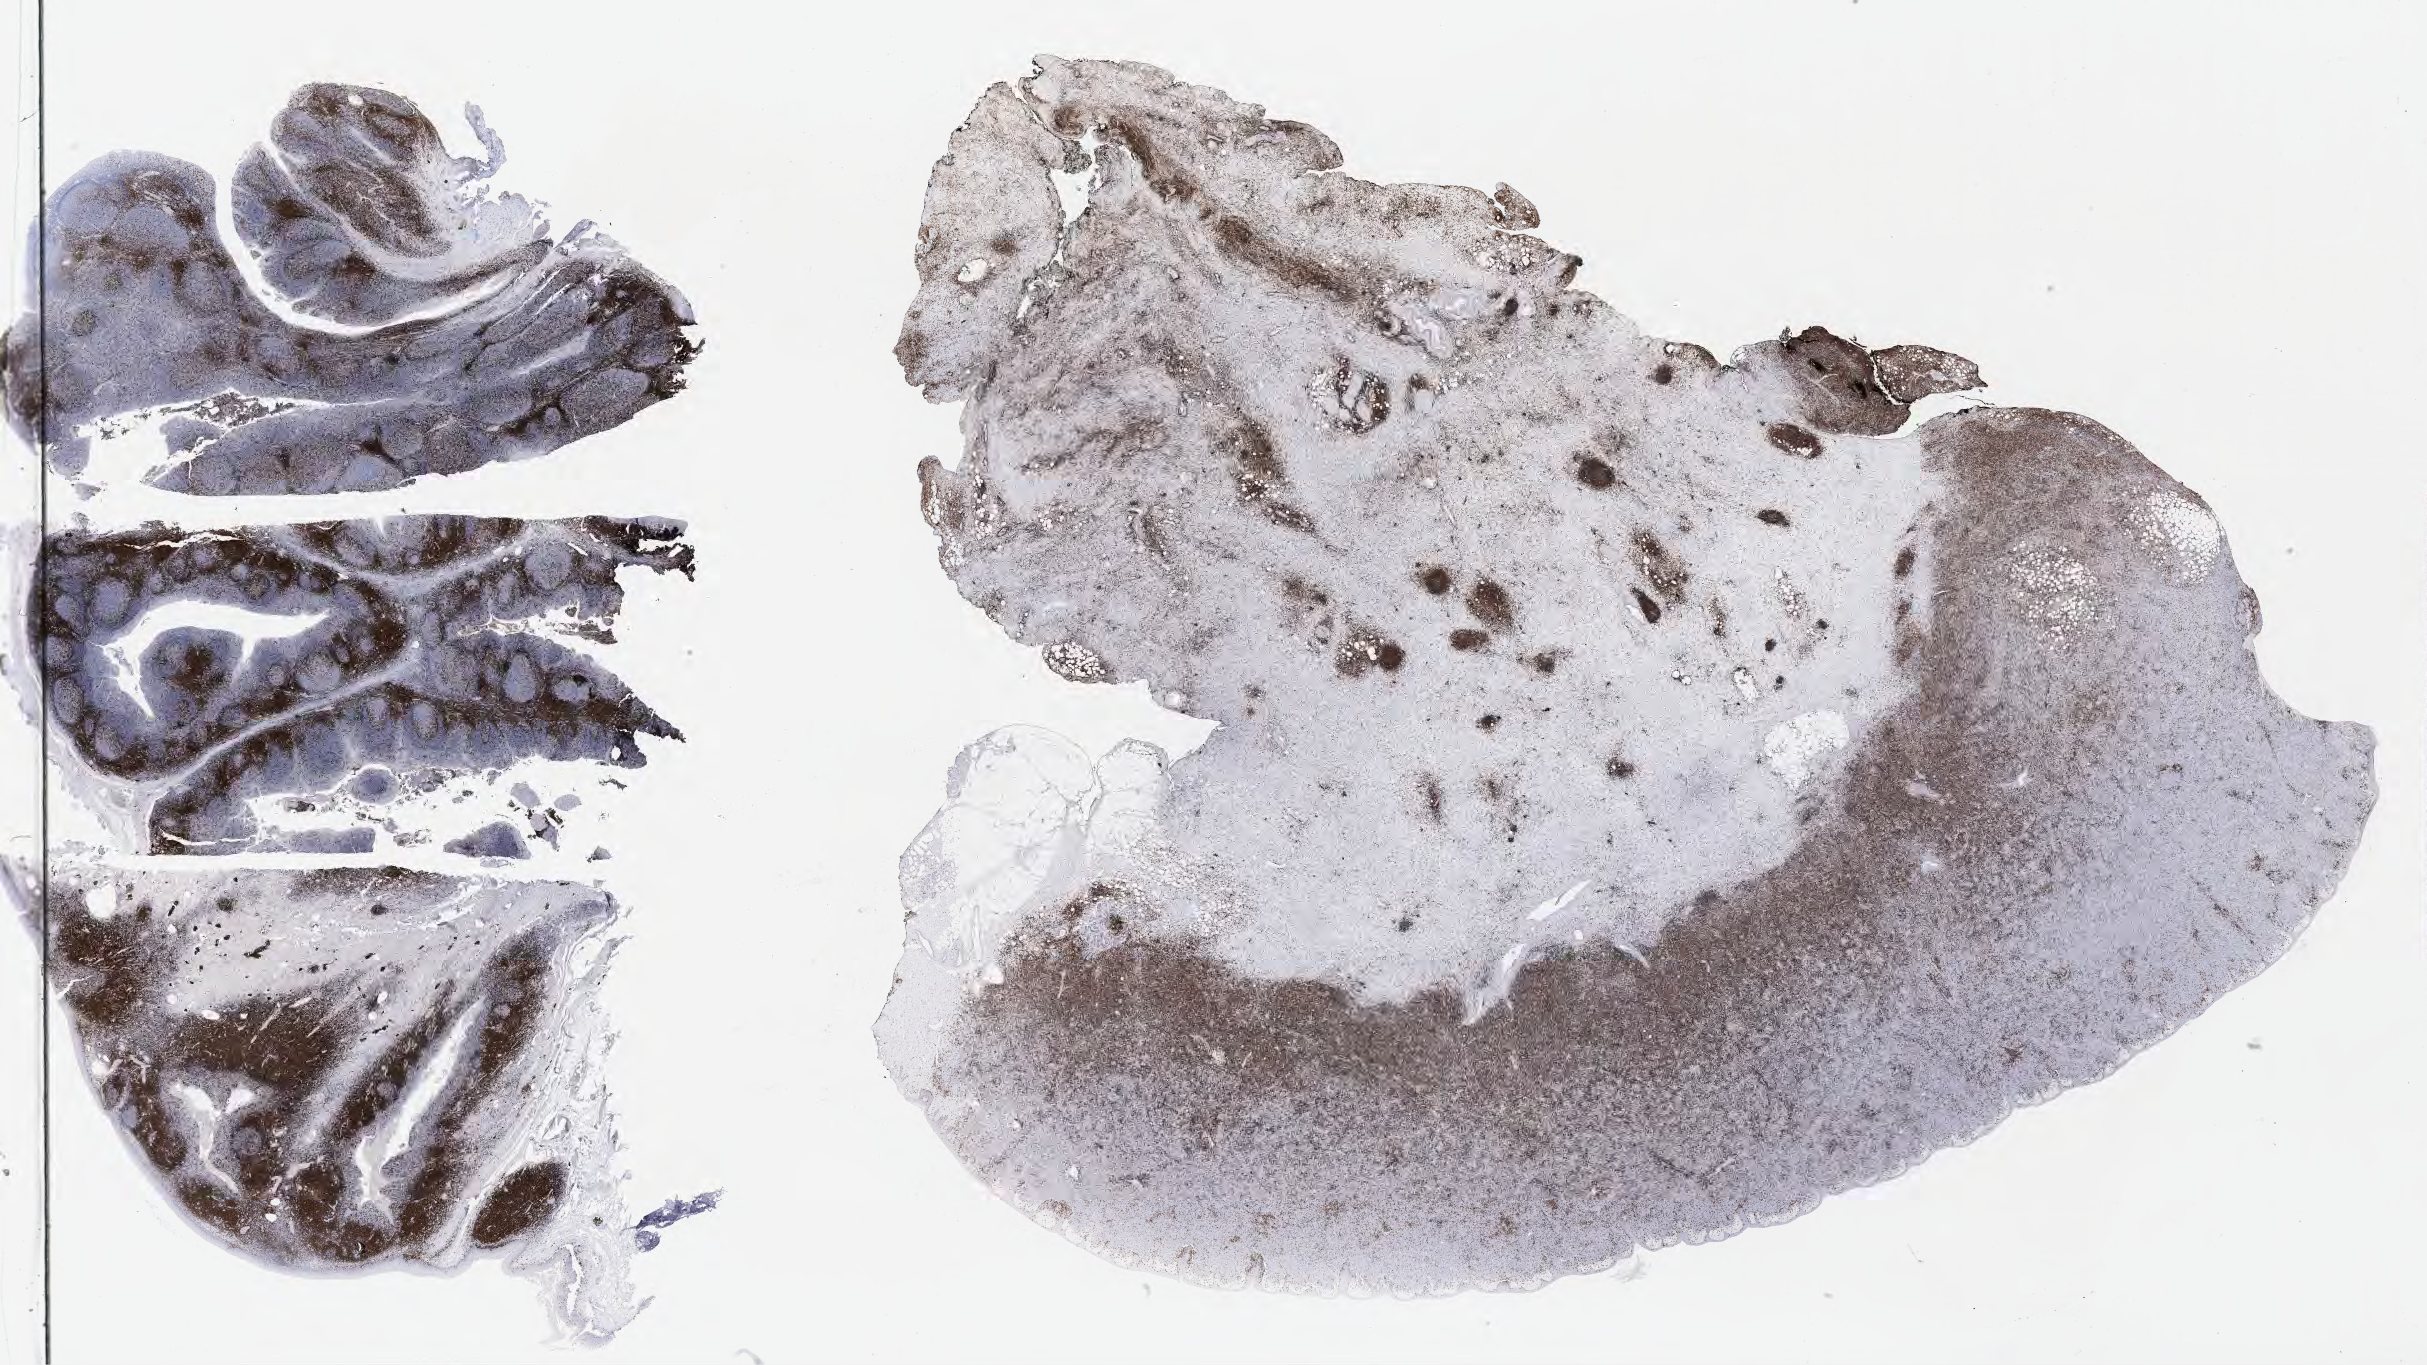
Whole-slide image, immunohistochemical stain for CD3 — a low-resolution overview of the entire scanned area, about 39.2 x 22.1 mm; tumor tissue; anatomic site: lymph node. Patient: male, age 52 years.
Histologic diagnosis: Diffuse large B-cell lymphoma, NOS.